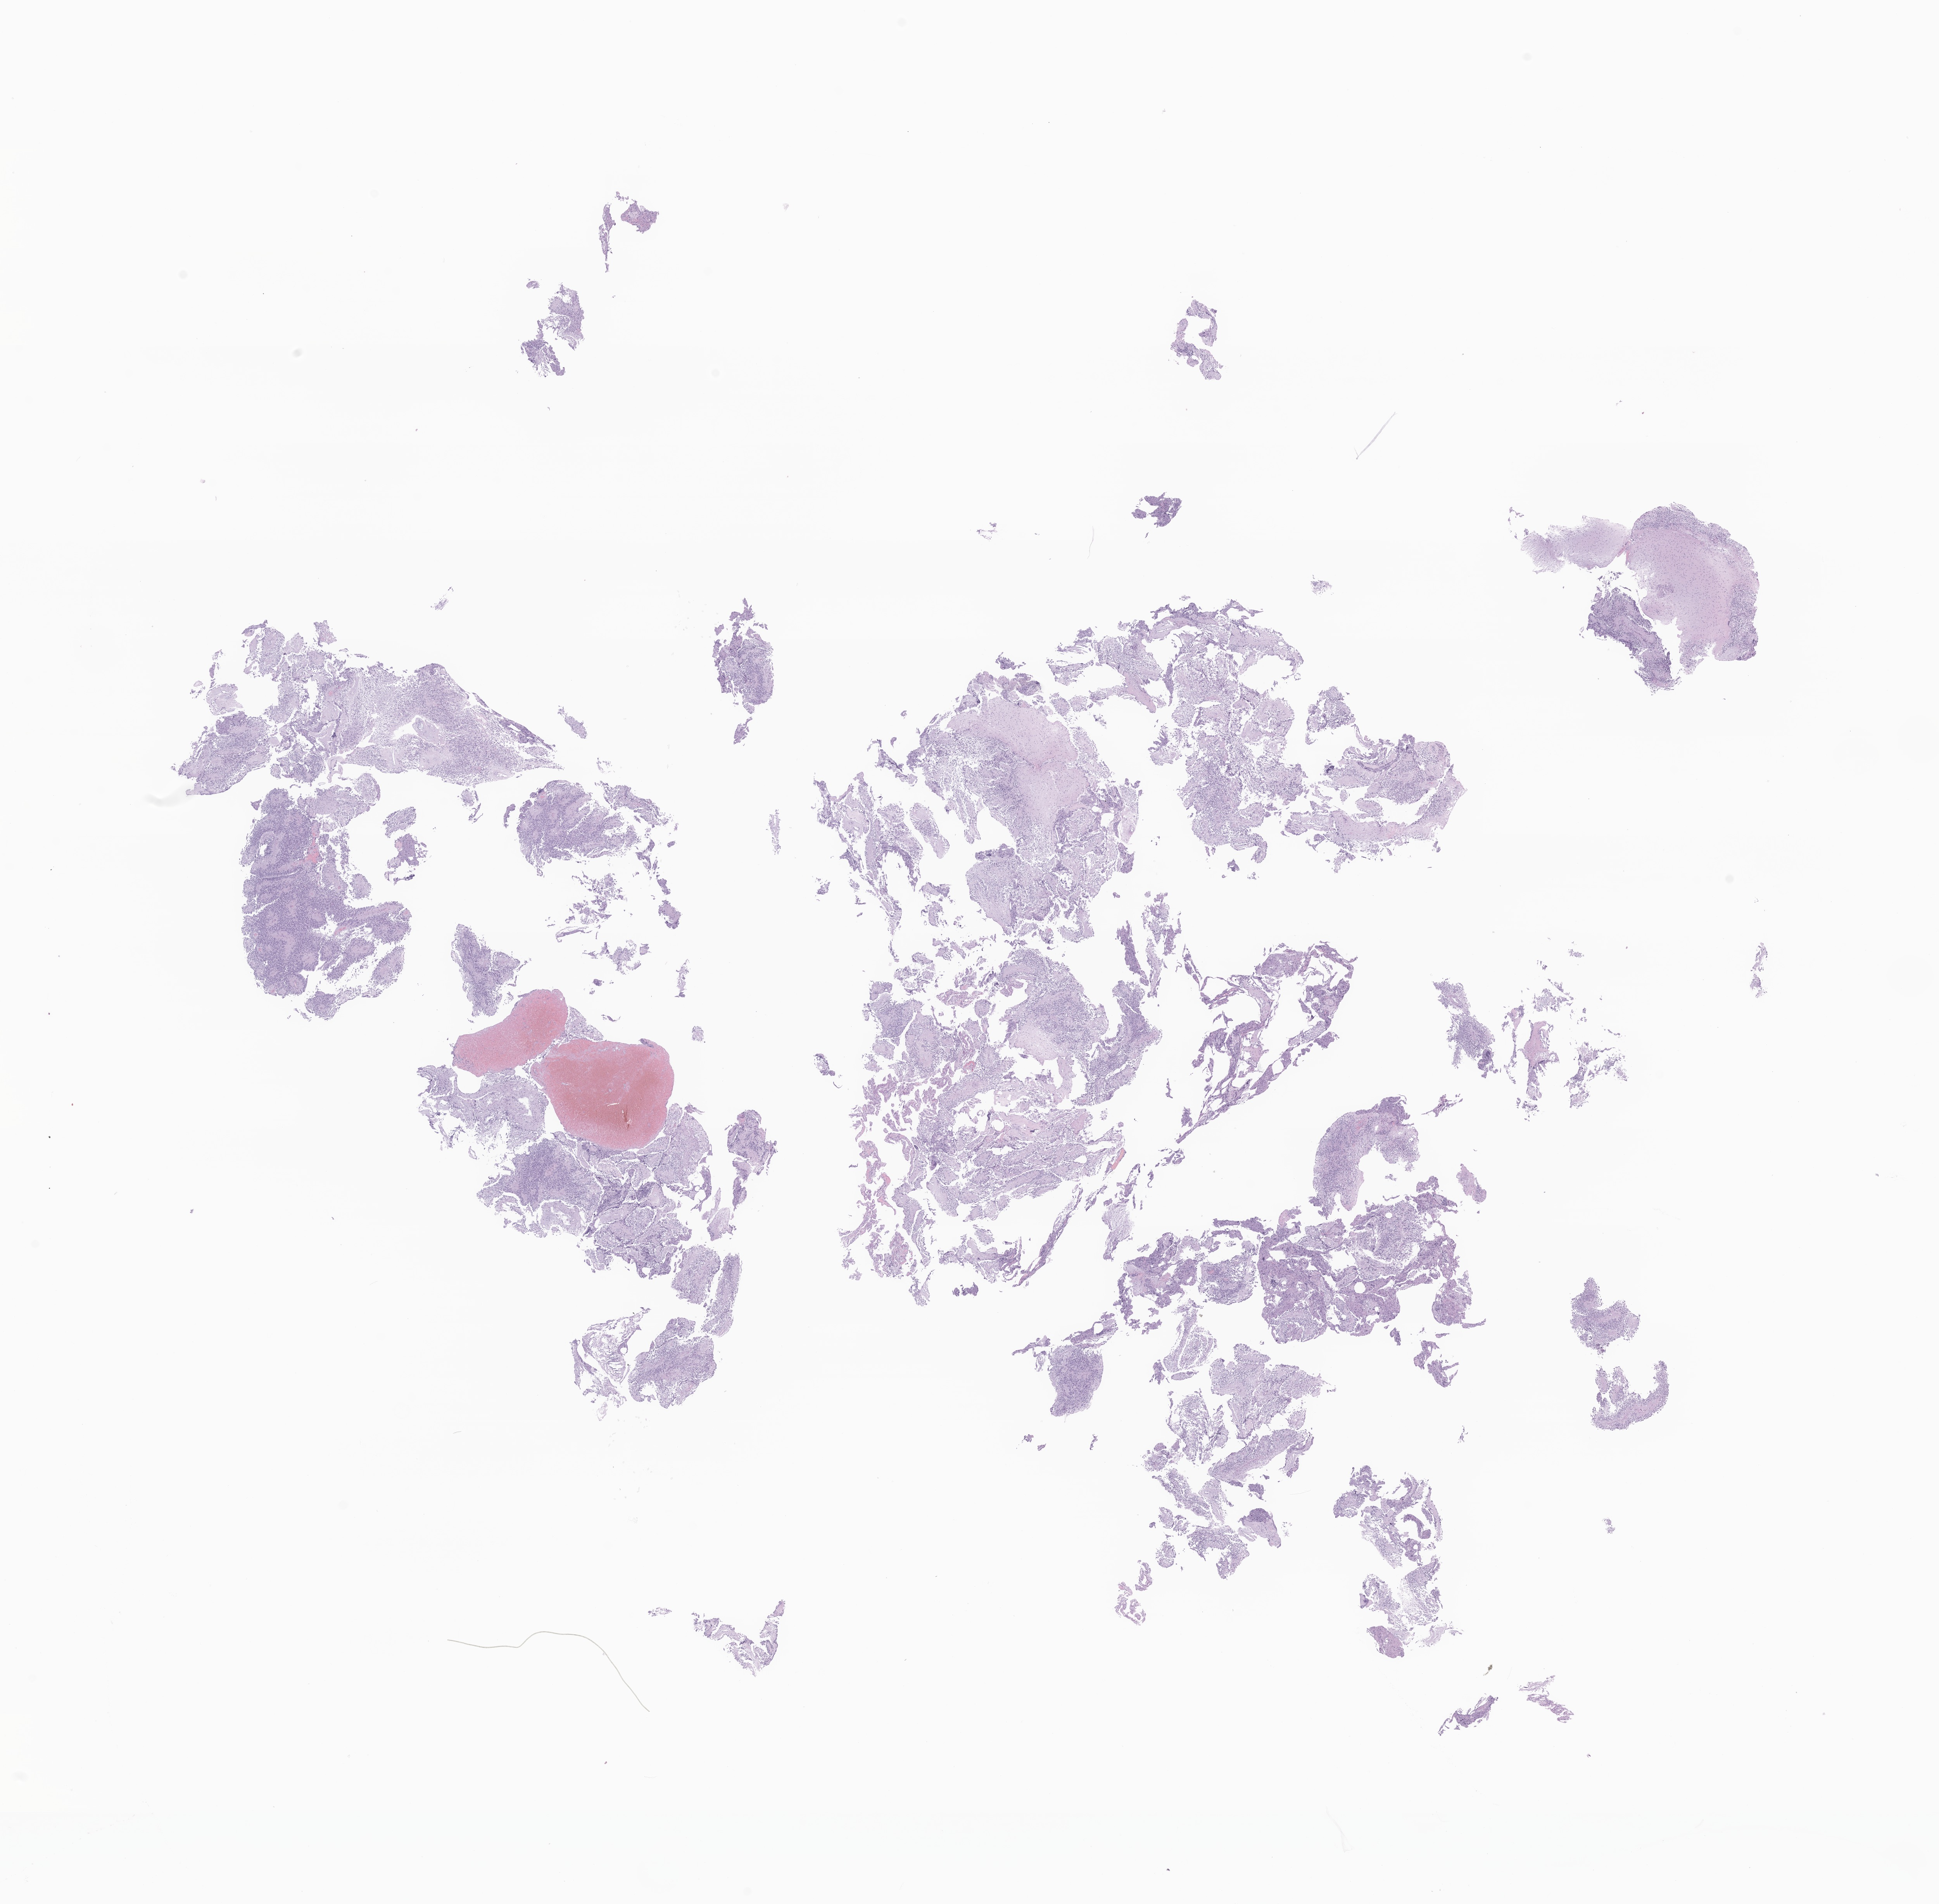
Whole-slide image, hematoxylin and eosin (H&E) stain of tumor tissue from the brain, a low-resolution overview of the entire scanned area, about 20.9 x 20.6 mm; formalin-fixed paraffin-embedded section. Patient male; age 160 months.
Diagnosis (ICD-O-3 morphology term): Ependymoma, NOS.